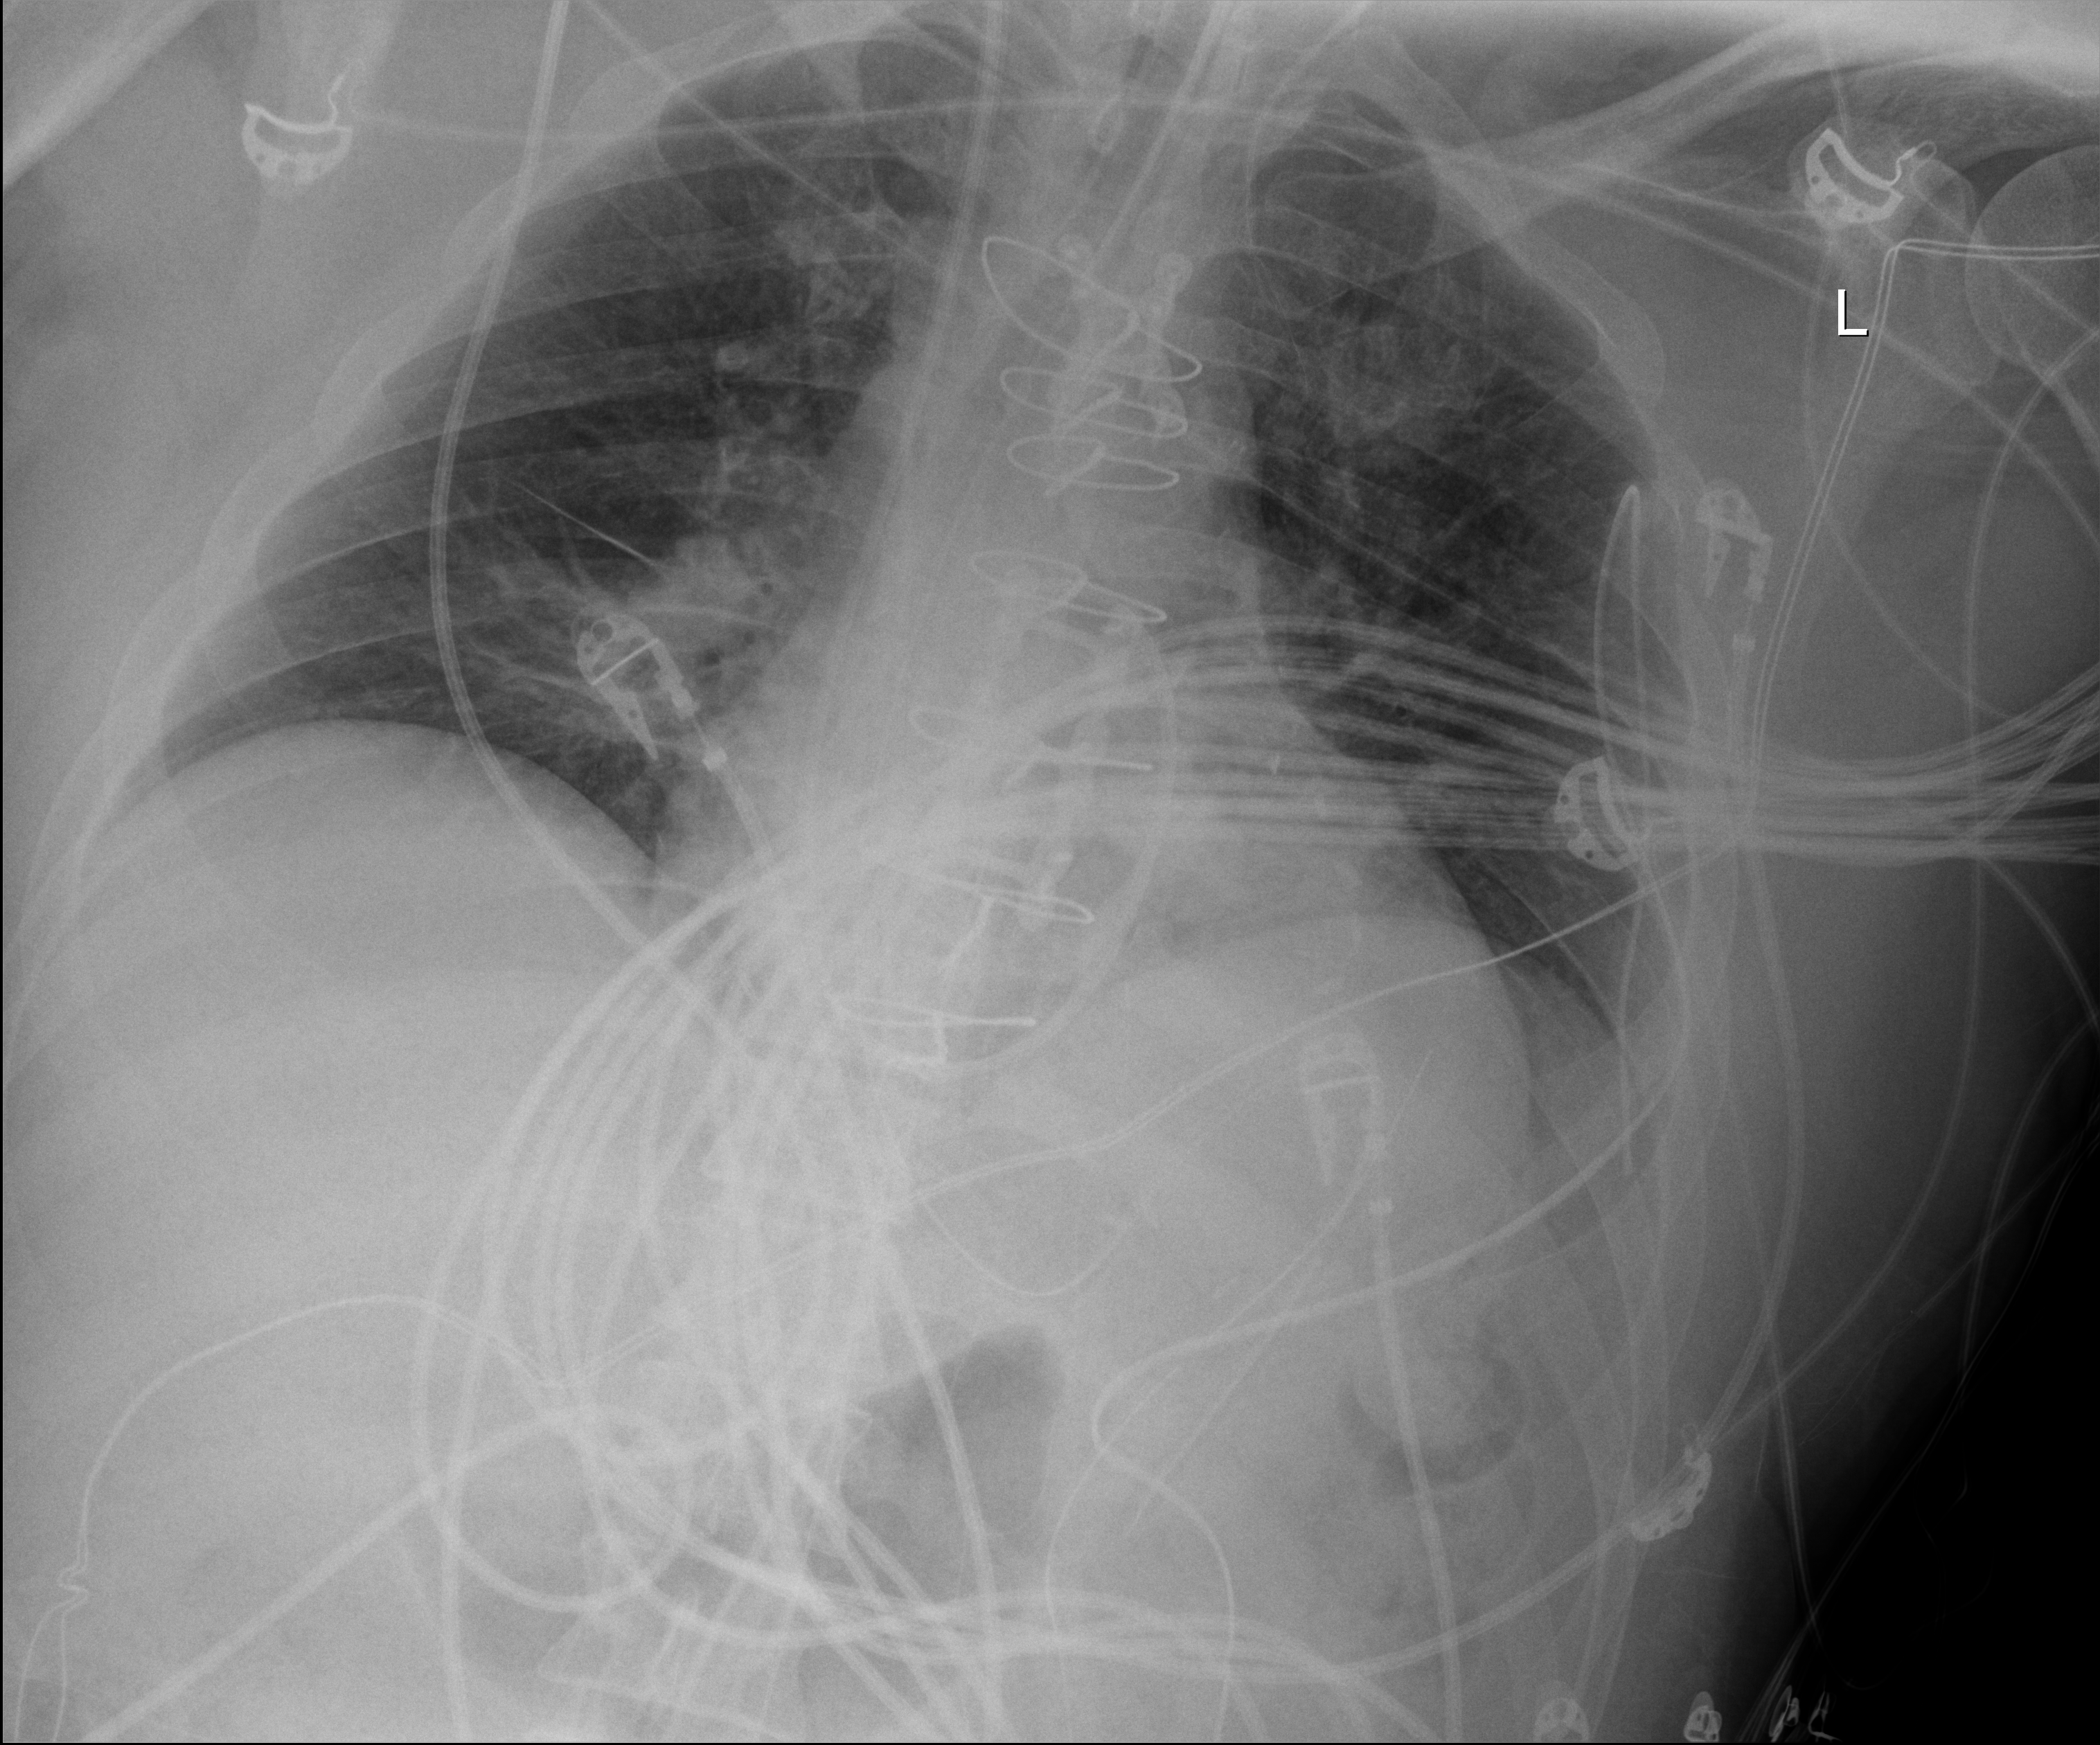
Bedside chest radiograph (digital radiography); anteroposterior (AP) projection. Patient hospitalised with COVID-19; male, aged 18–59 years.
From the hospital-stay record, not from the radiograph (when in the stay this image was taken is not recorded):
- mechanically ventilated during this hospital stay: no